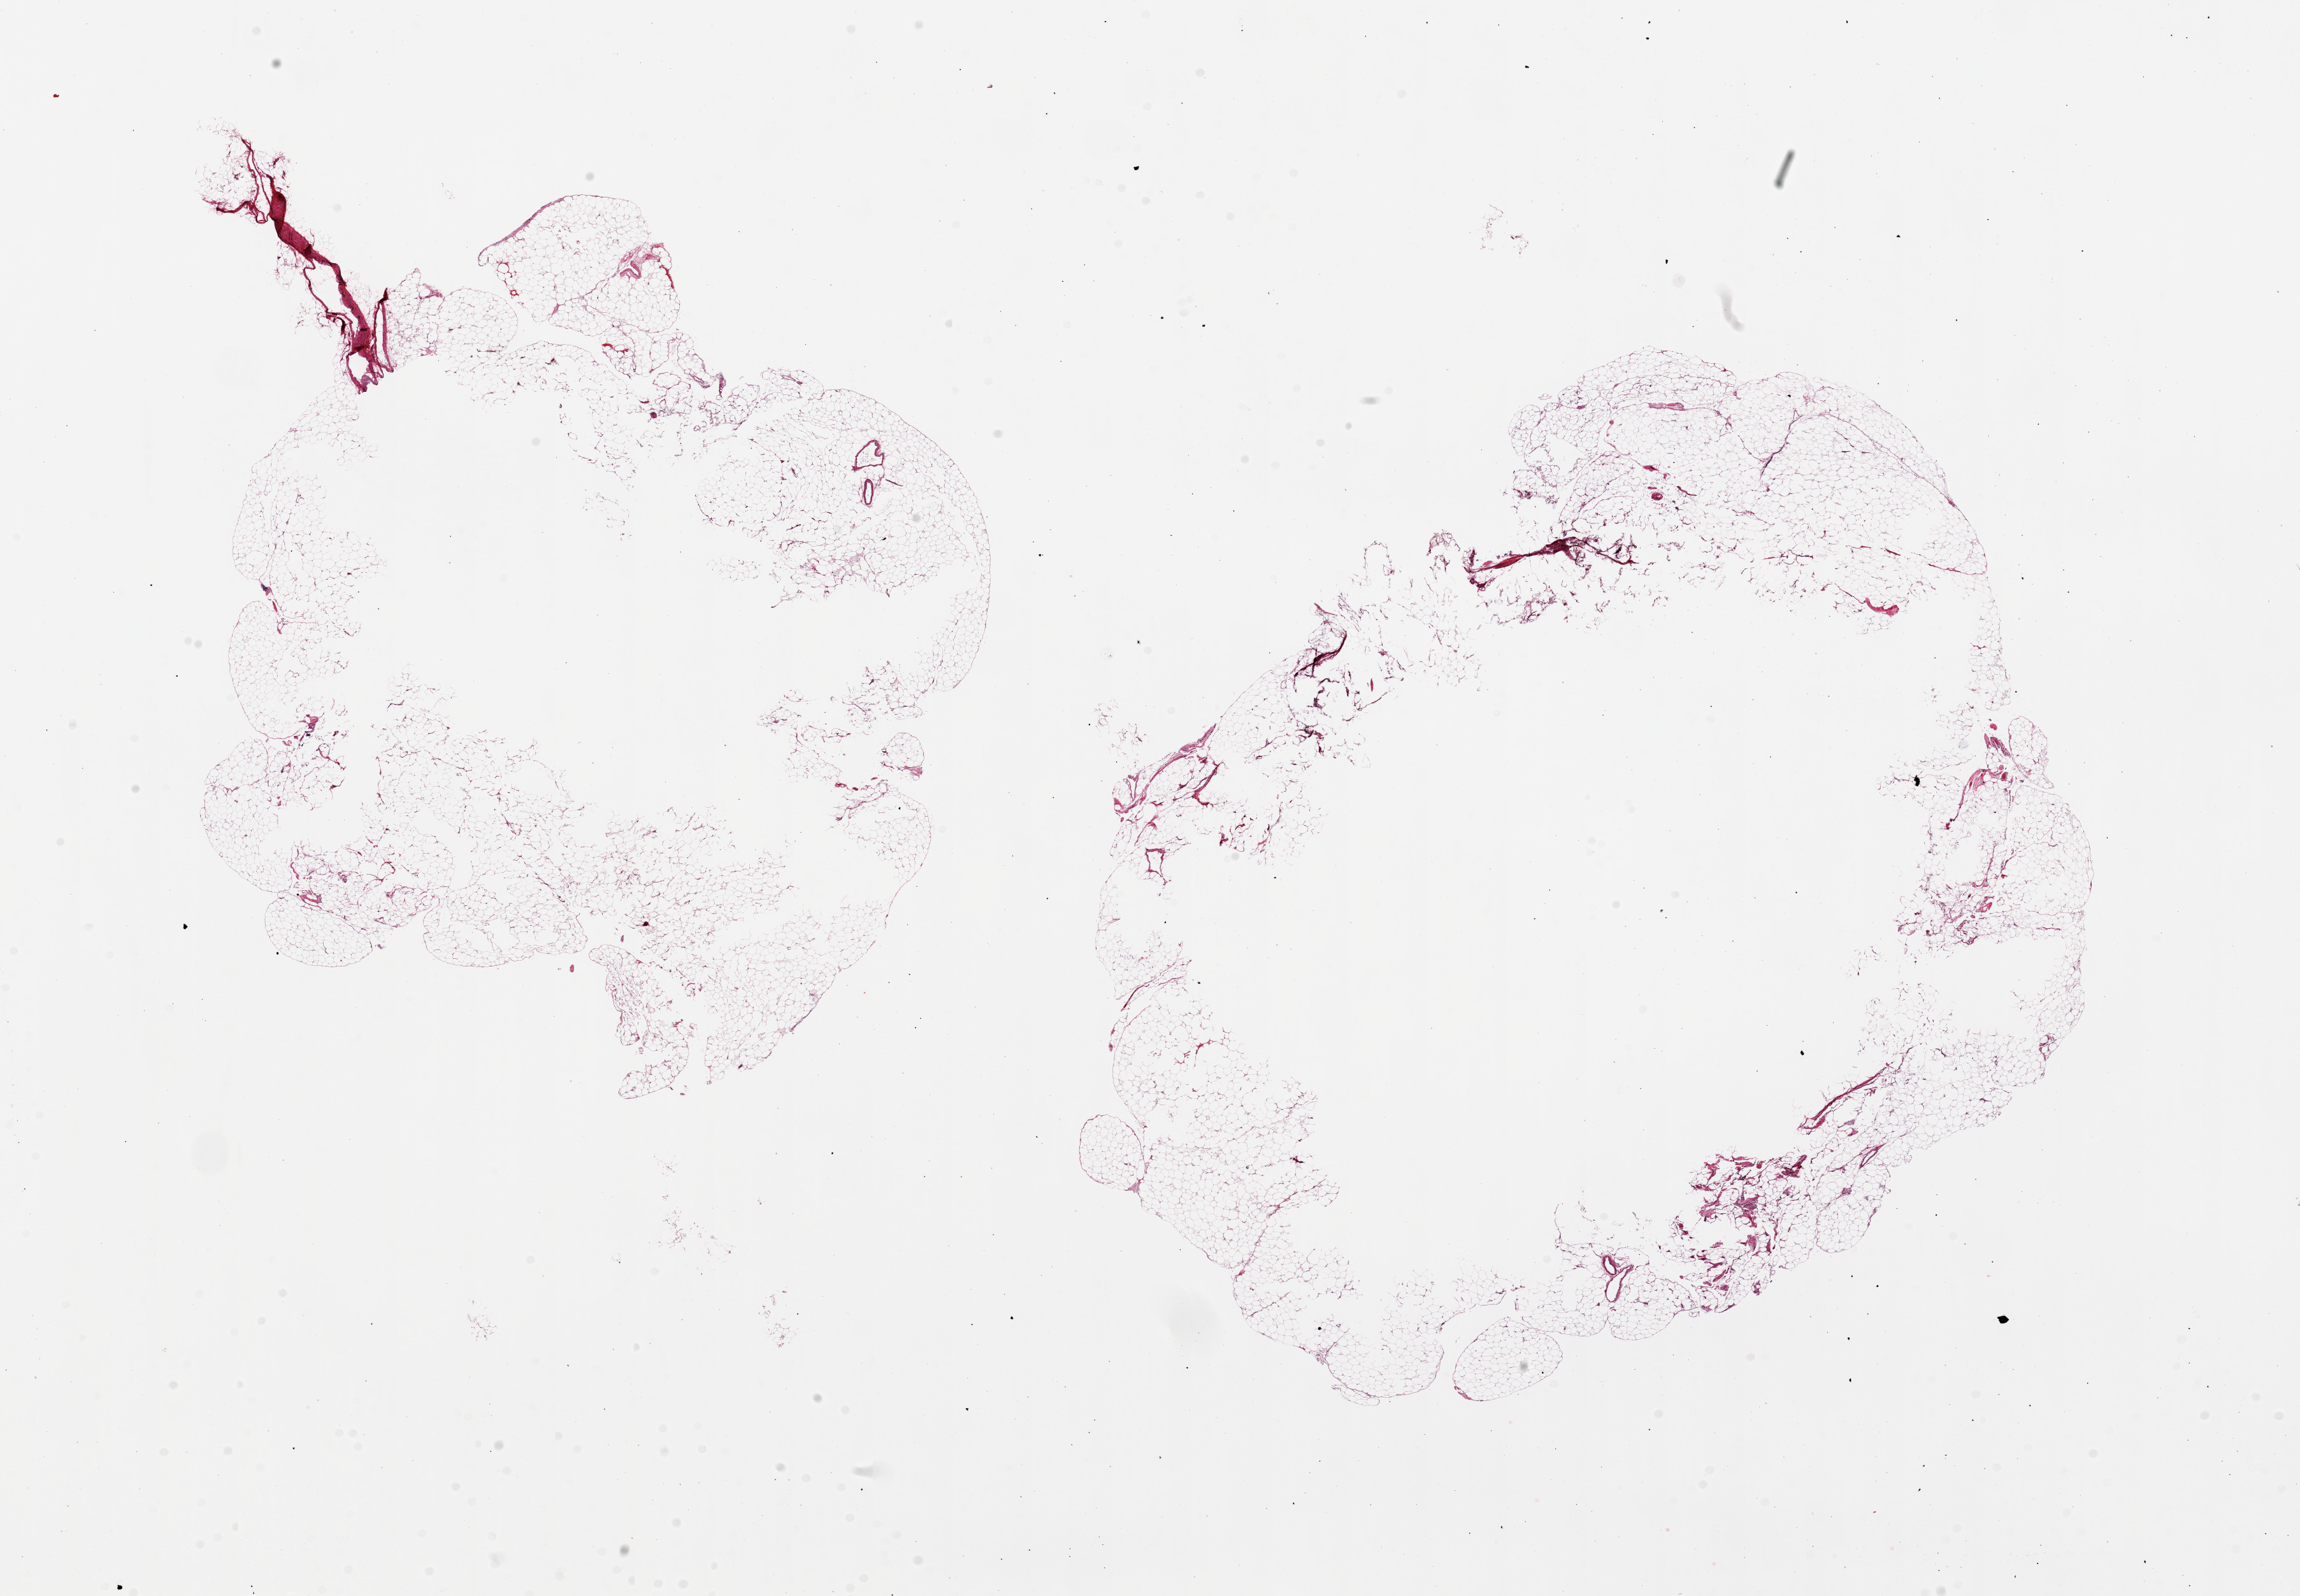
Digitized H&E-stained section — a low-resolution overview of the entire scanned area, about 28.5 x 19.8 mm (slide scanned at 20x), PAXgene-fixed paraffin-embedded (PFPE) section, target tissue: omentum, donor tissue sample. Male donor.
* pathologist's review note for this sample: 2 pieces, 13x10 and 9x9mm; multiple penetrating small vessels